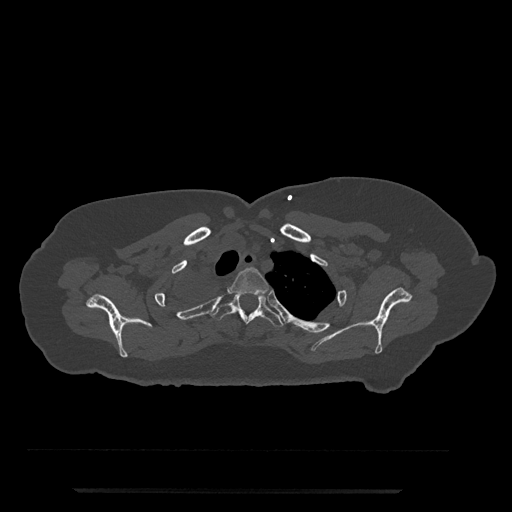
CT including the spine, one axial slice; slice 648 of 797 in the series (ordered by position); 120 kVp; bone window (W 1800 / L 400 HU); 0.5 mm slice thickness; 512 × 512 image matrix, field of view 440 × 440 mm. Female patient, age 51 years. Case-level facts recorded for this patient, not image findings: primary cancer: neuro.
Structures marked on this image (semi-automatic segmentation, software-assisted and operator-edited):
- T2 vertebra: box from (x=228, y=267) to (x=269, y=296) px
- T3 vertebra: (x=211, y=293)–(x=284, y=327)